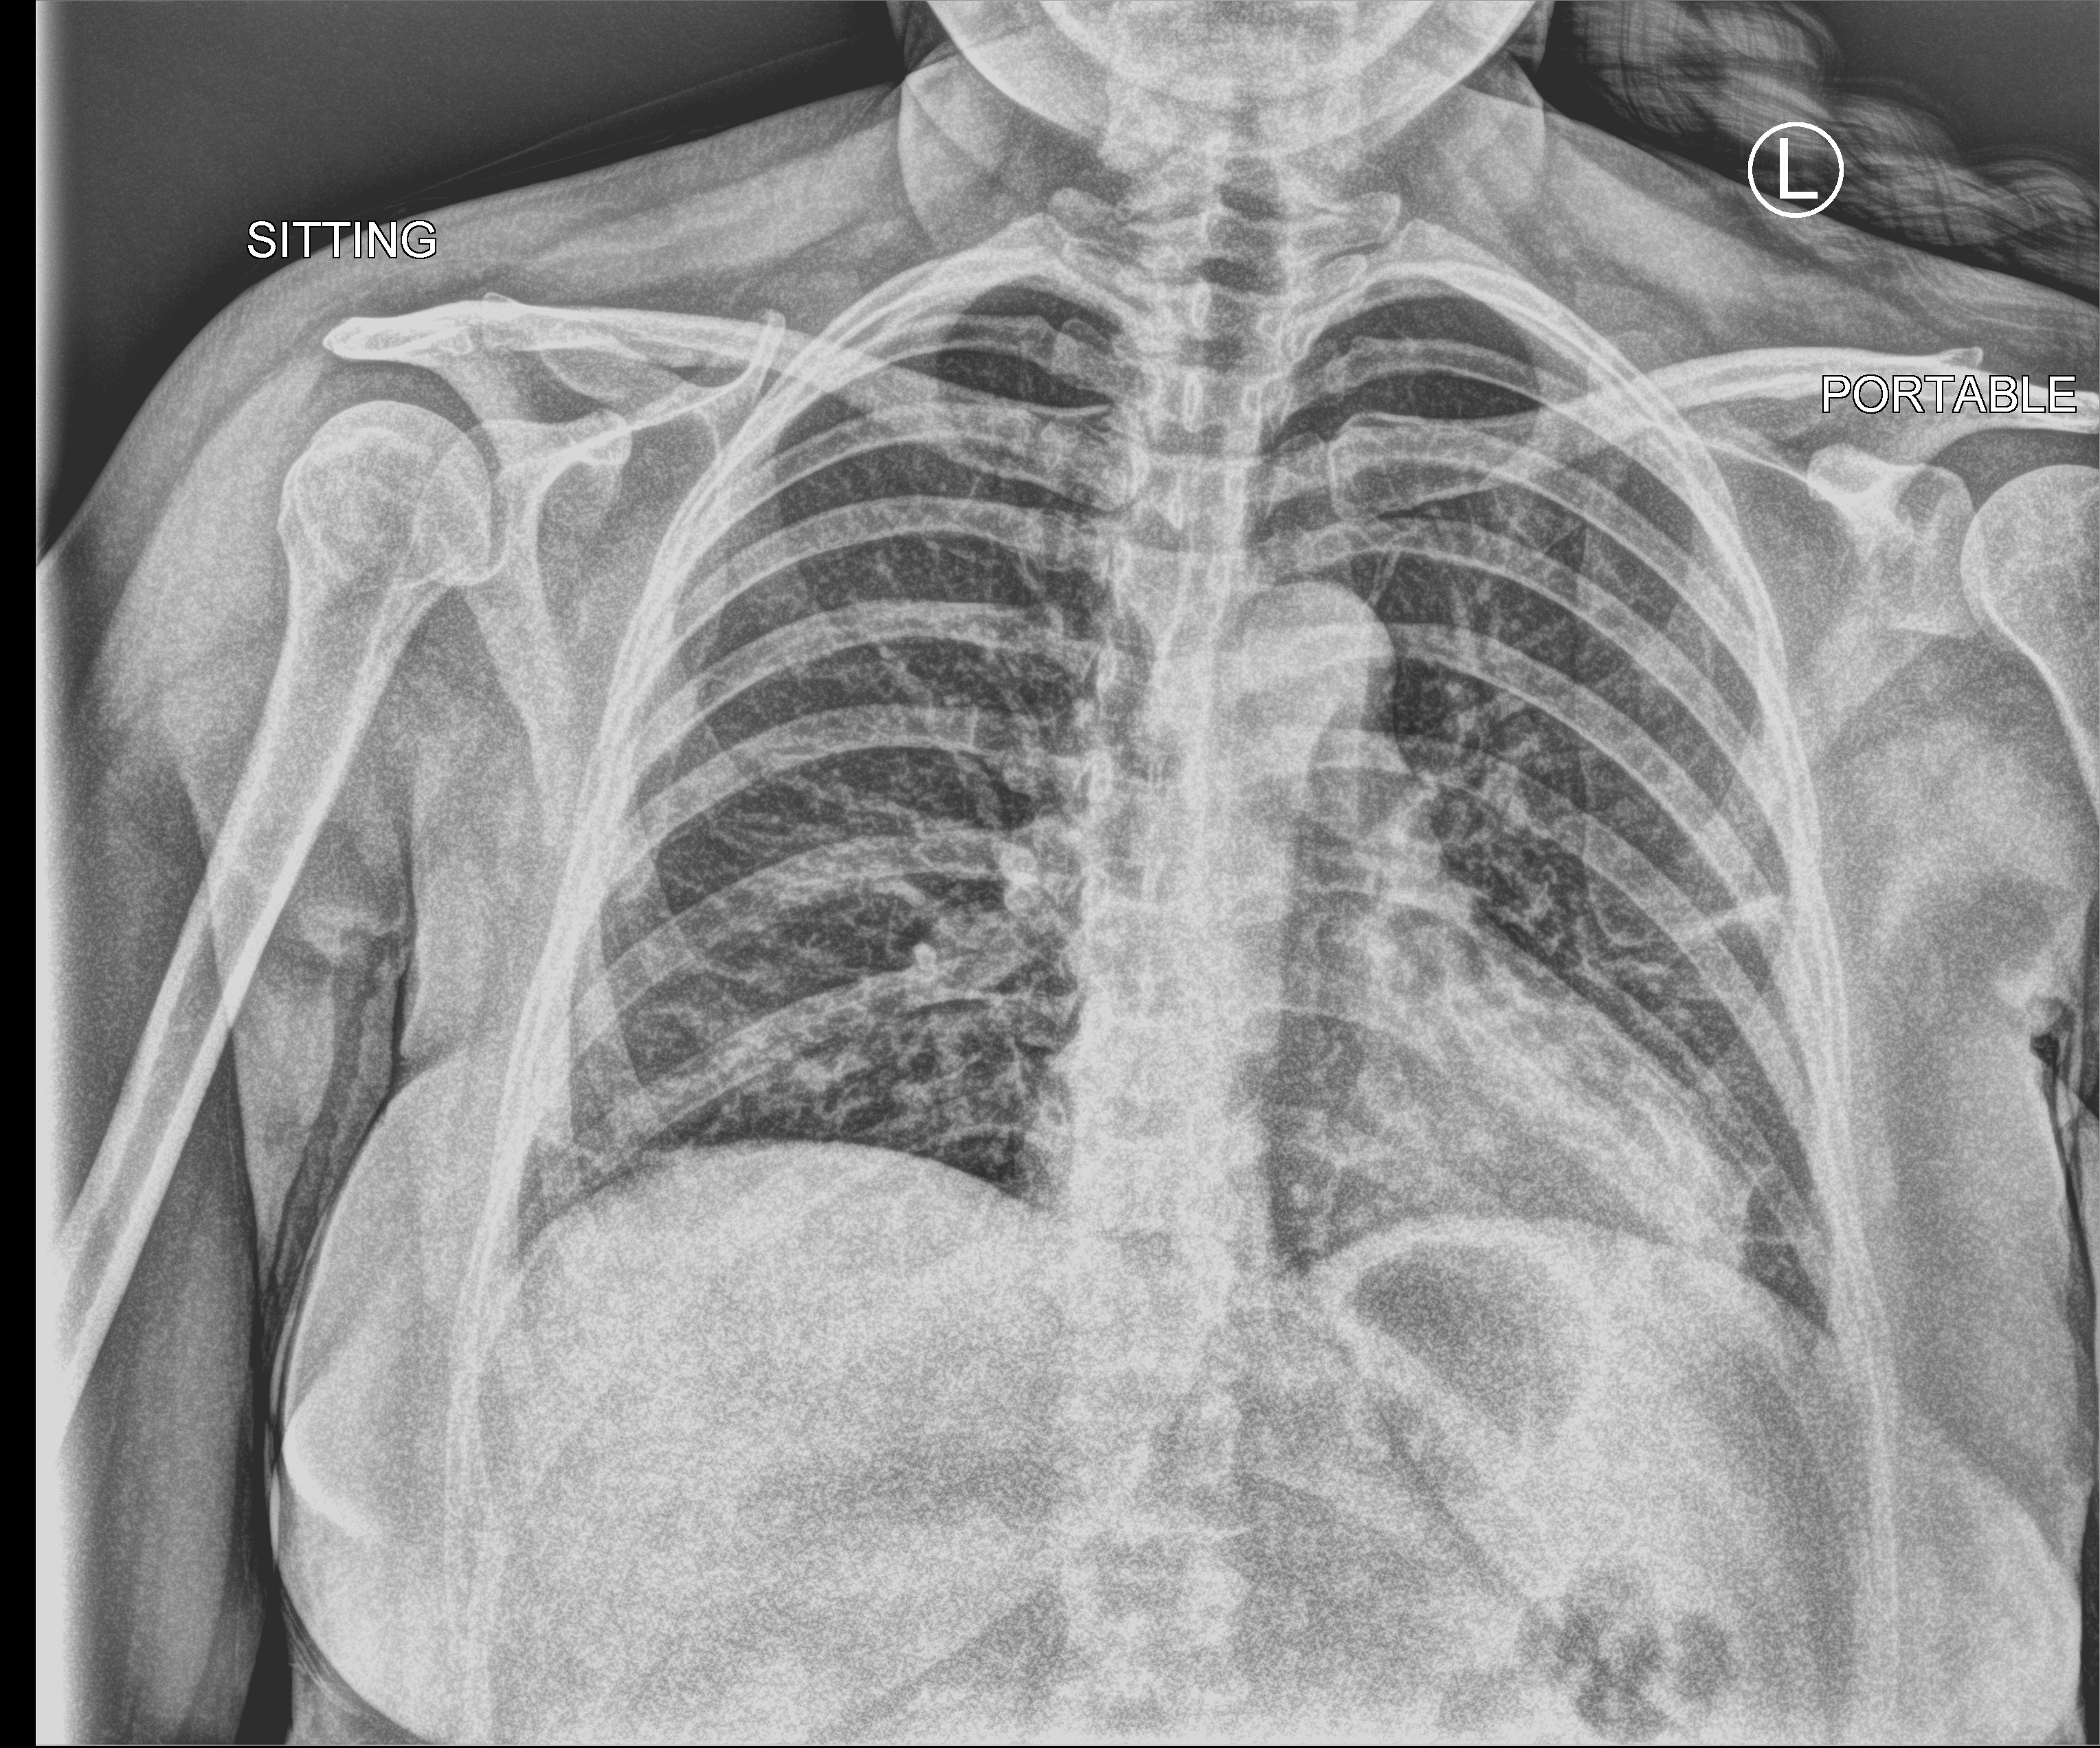
Chest X-ray (portable), anteroposterior (AP) projection. Patient hospitalised with COVID-19; female, aged 18–59 years.
From the hospital-stay record, not from the radiograph (when in the stay this image was taken is not recorded): admitted to intensive care during this hospital stay: no.